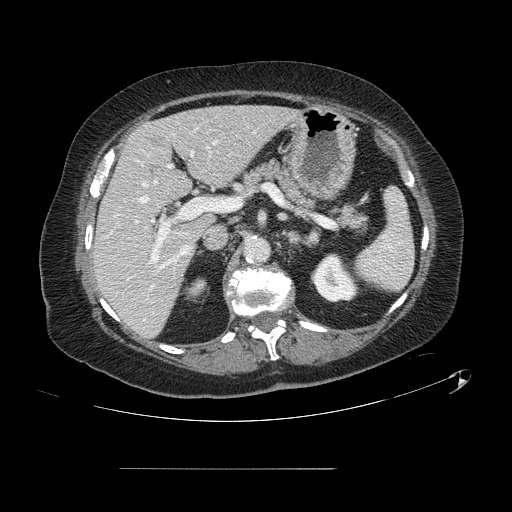
Contrast-enhanced abdominal CT, one axial slice. Slice 72 of 148 in the series (ordered by position). Intravenous contrast given. Soft-tissue window (W 400 / L 40 HU). 512 × 512 image matrix, field of view 439 × 439 mm. Female patient, age 75 years. Case-level facts recorded for this patient, not image findings: diagnosis: colorectal cancer liver metastases, imaged before liver resection; multiple liver metastases: no; largest metastasis: 2.4 cm; disease in both lobes: no.
Structures marked on this image (manually delineated by an expert):
- hepatic veins: bounding box [x1, y1, x2, y2] px = [140, 141, 216, 255]
- liver: [94, 106, 294, 337]
- planned liver remnant (the part of the liver to remain after resection): [94, 106, 293, 337]
- portal vein (with intrahepatic branches): [135, 153, 209, 268]
- liver metastasis: [152, 140, 158, 145]